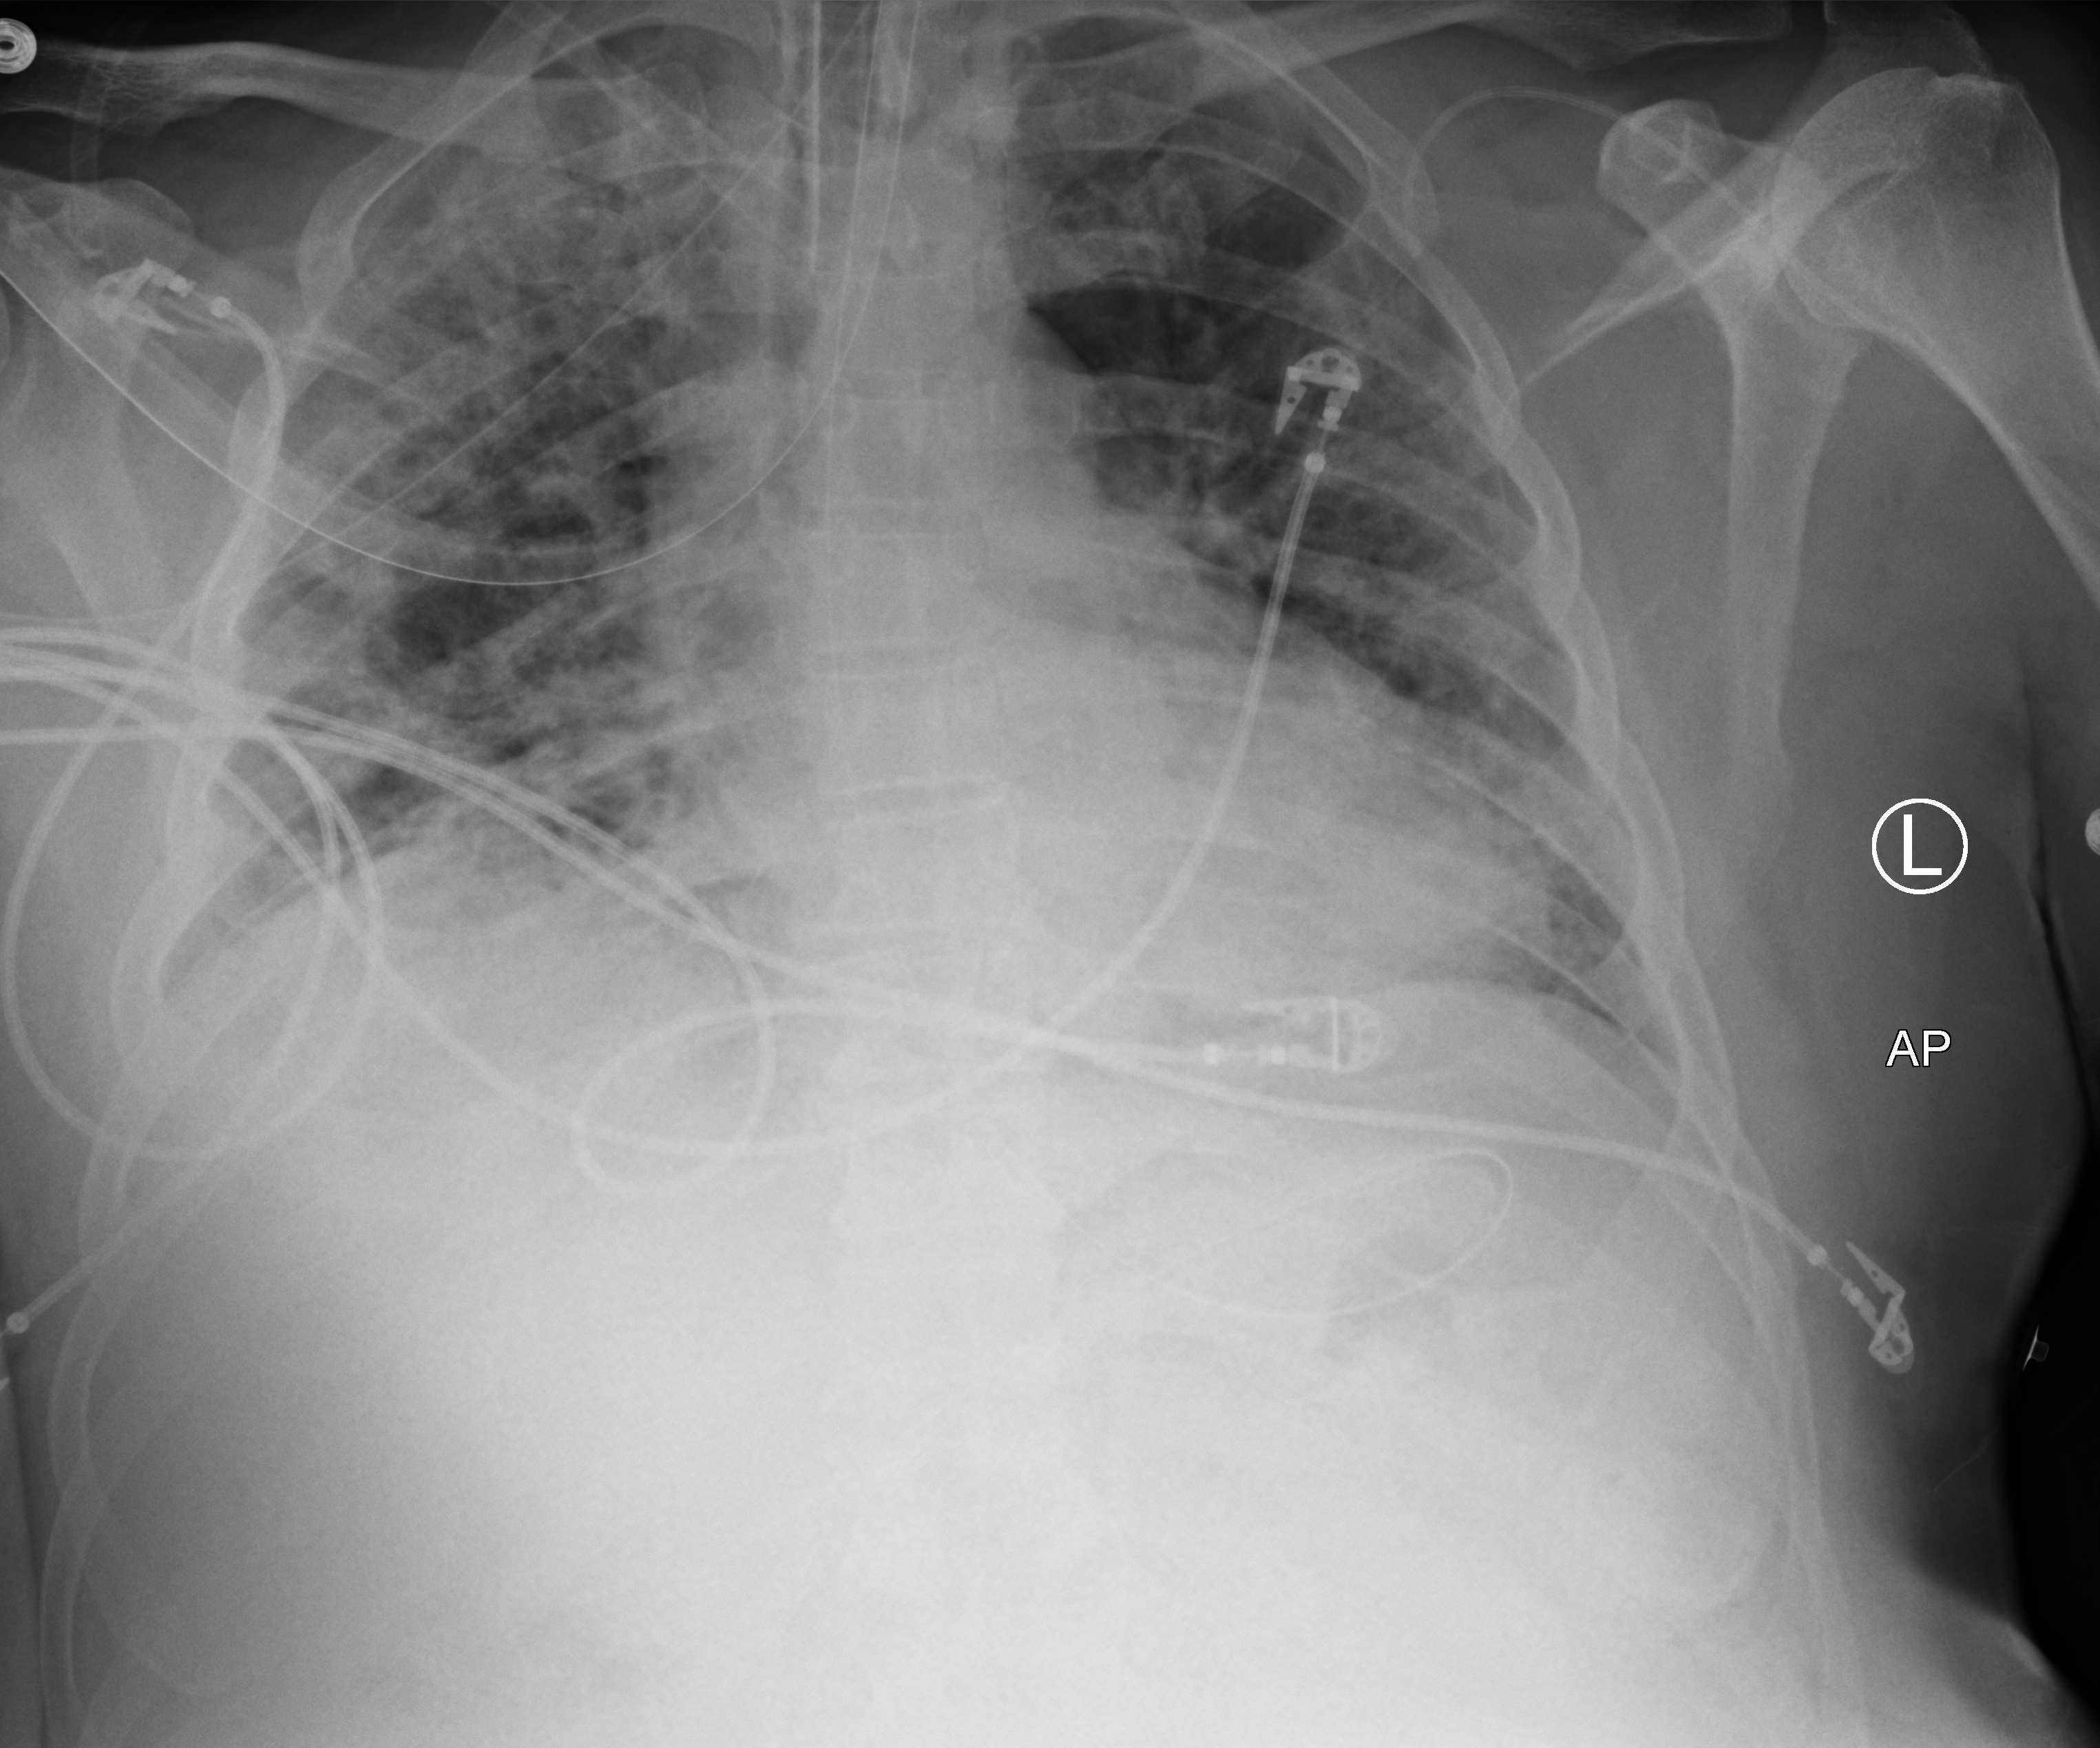
Chest X-ray (portable); anteroposterior (AP) projection. Patient hospitalised with COVID-19; male, aged 18–59 years.
From the hospital-stay record, not from the radiograph (when in the stay this image was taken is not recorded): mechanically ventilated during this hospital stay: yes.